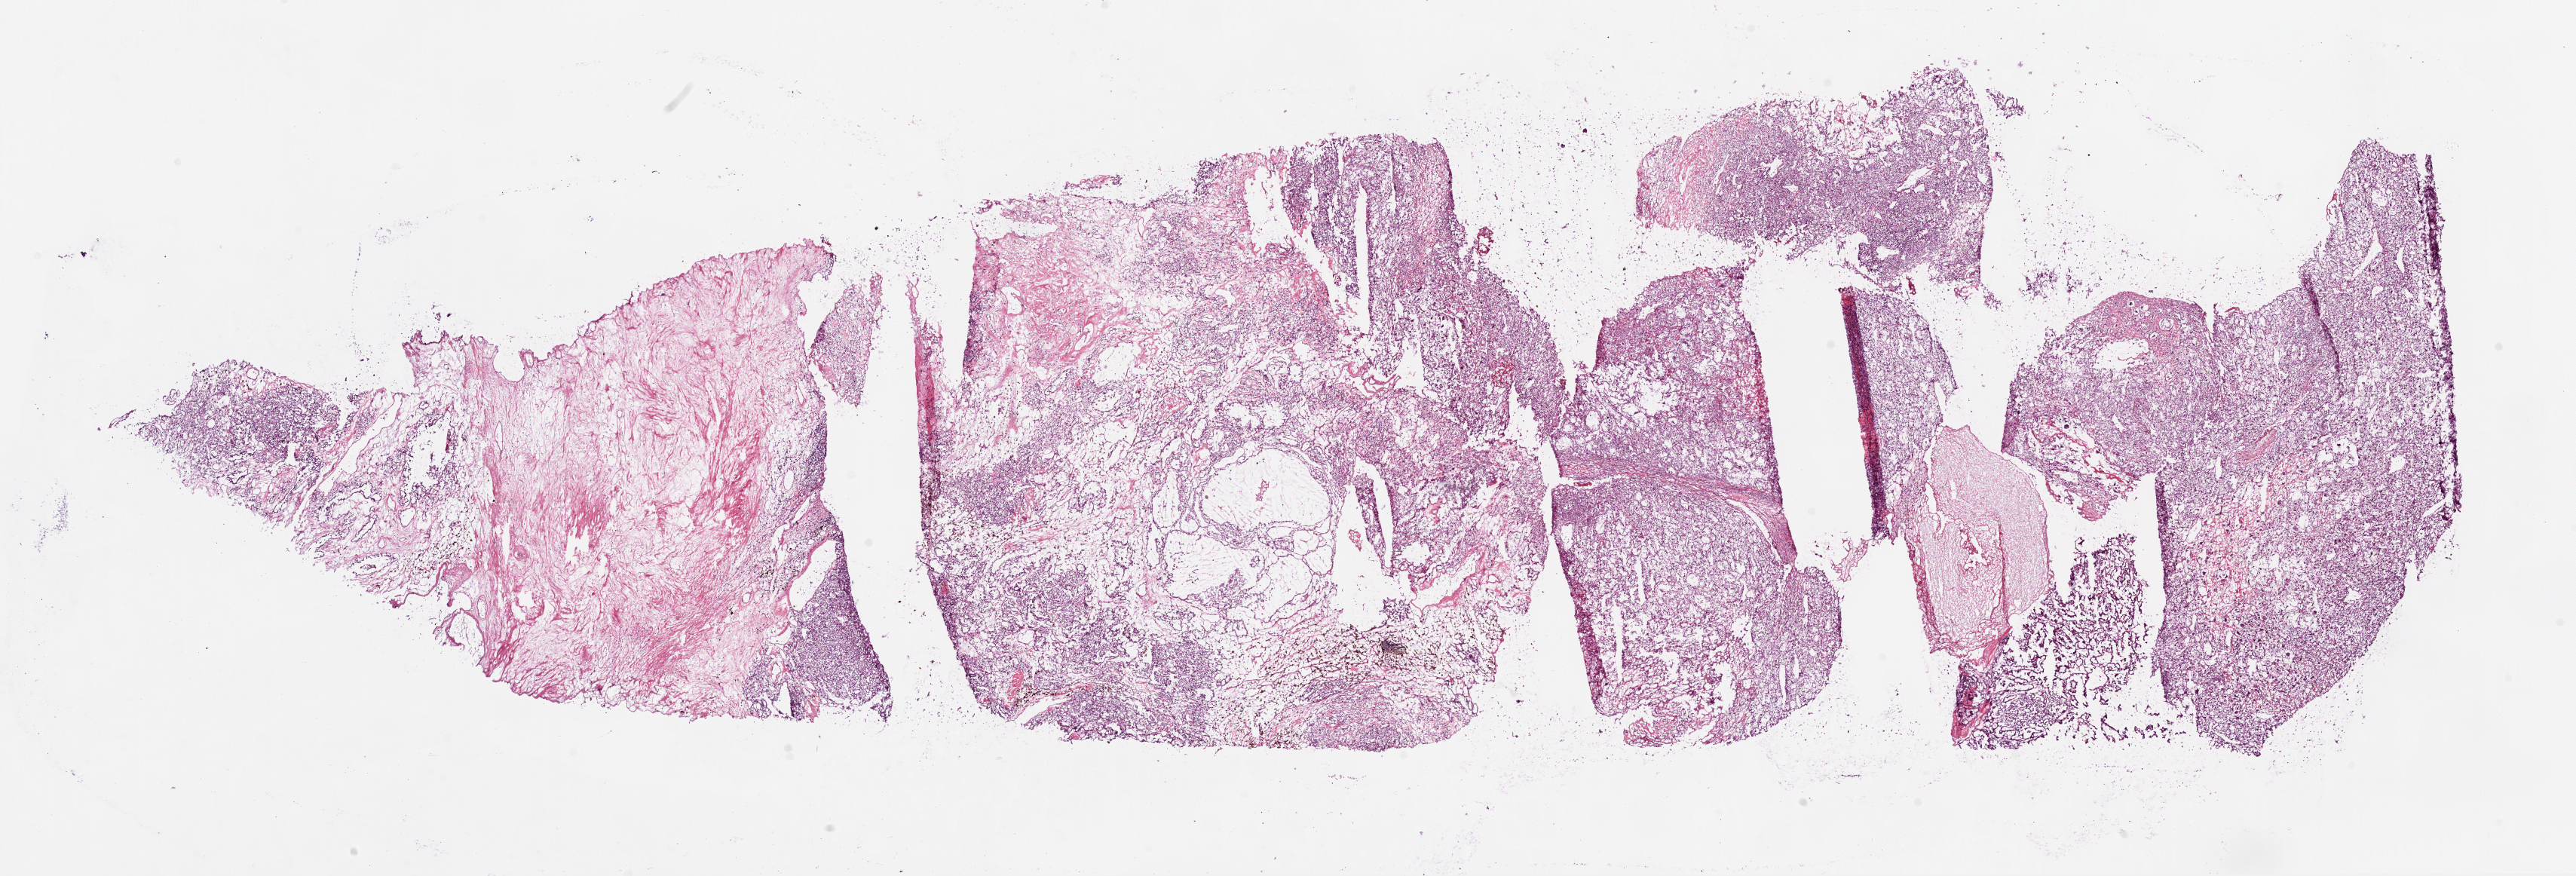
Digitized H&E-stained tissue section (whole slide) — low-resolution overview of the scanned area, about 27.6 x 9.4 mm (from a 20x scan), frozen section from the top of the tissue portion, kidney, primary tumour sample. Patient sex: male. Histologic grade: G4 (undifferentiated). Composition of this section per pathologist review: tumour cells 80%, tumour nuclei 75%, normal cells 0%, stromal cells 20%, necrosis 0%. Inflammatory infiltration, as recorded: lymphocyte infiltration 10%, monocyte infiltration 2%, neutrophil infiltration 0%.
Diagnosis: Clear cell adenocarcinoma, NOS. AJCC pathologic stage: I. TNM: T1b NX M0. Laterality: left.